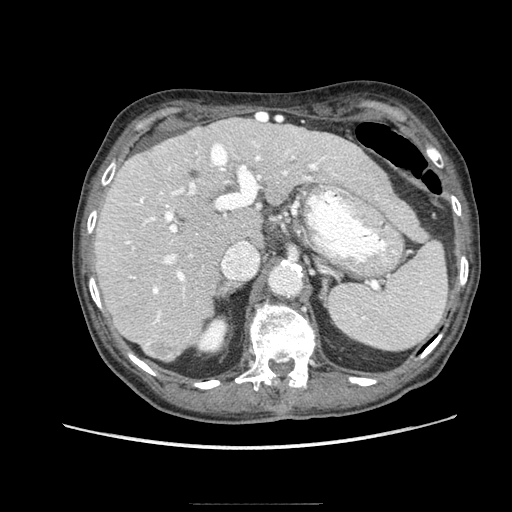
Contrast-enhanced abdominal CT (liver protocol), one axial slice; slice 55 of 83 in the series (ordered by position); reconstruction kernel STANDARD; 140 kVp; soft-tissue window (W 400 / L 40 HU); 2.5 mm slice thickness; 512 × 512 image matrix, field of view 360 × 360 mm. Case-level facts recorded for this patient, not image findings: diagnosis: hepatocellular carcinoma (patient treated with transarterial chemoembolisation; whether this scan precedes or follows treatment is not stated here); TNM stage (as recorded): Stage-I.
Annotated regions visible in this slice (semi-automatic segmentation, software-assisted and operator-edited):
- liver parenchyma outside the tumour (the mass and vessels are separate outlines, so this box may not span the whole liver): bounding box <94,118,400,360> (left, top, right, bottom; pixels)
- mass: <143,333,179,360>
- liver vessels: <100,119,337,325>